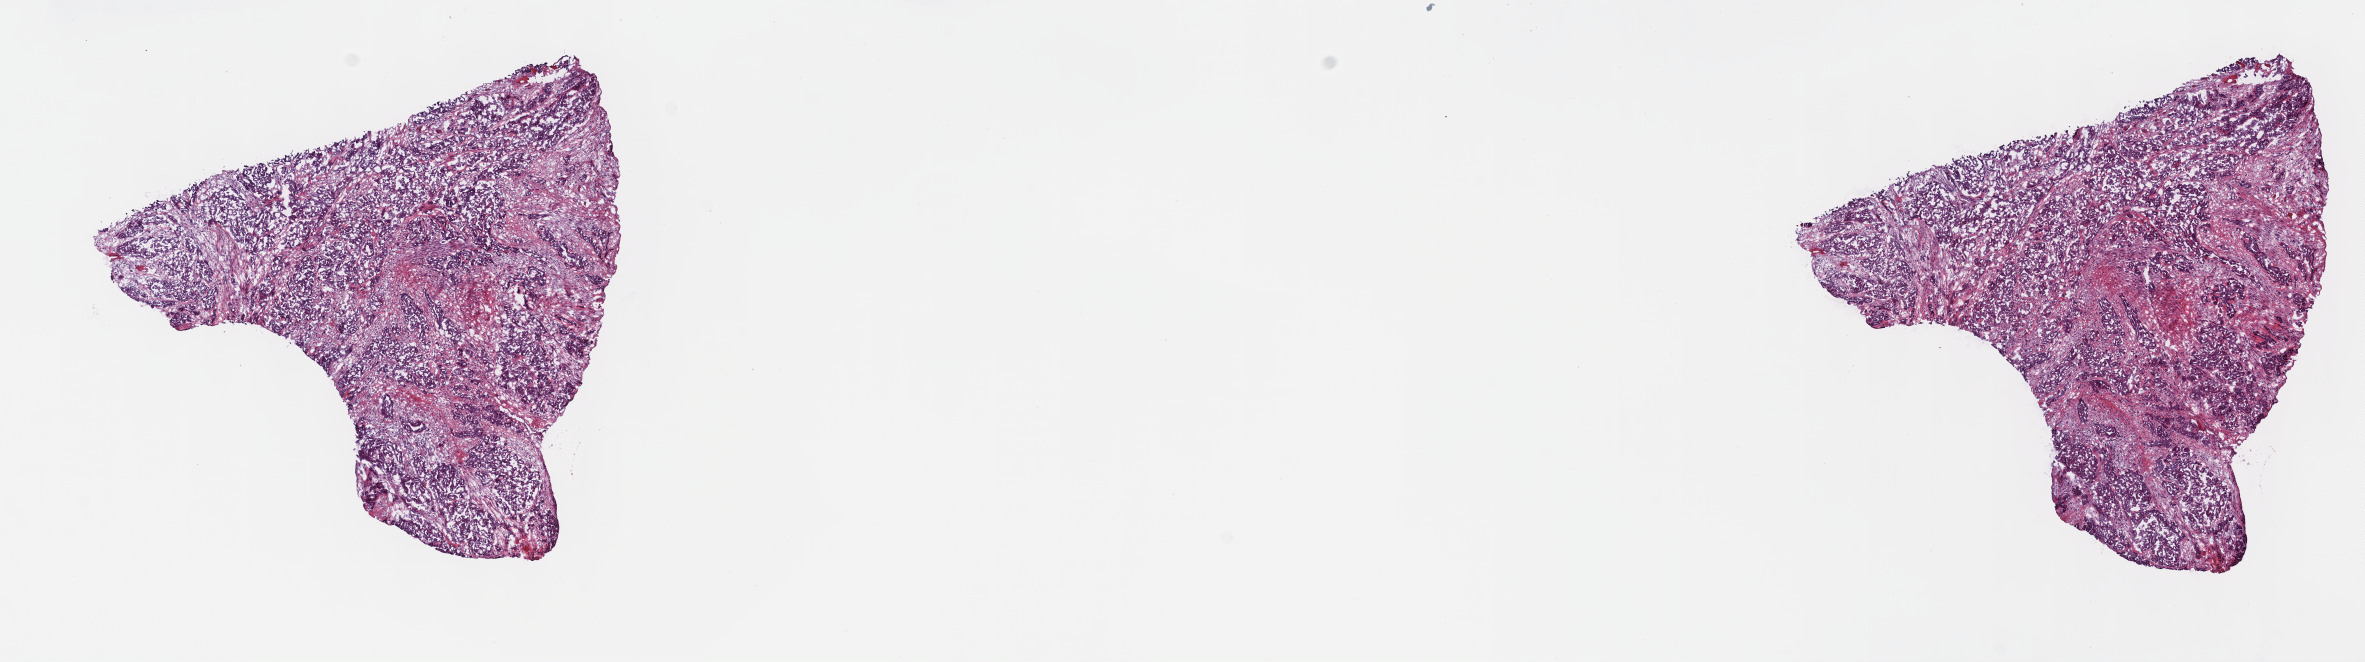
H&E-stained whole-slide image, shown as a low-resolution overview of the whole scanned area (about 19.1 x 5.4 mm, from a 40x scan); frozen section from the top of the tissue portion; sample: primary tumour, mesothelium. Female, age 28 years at initial diagnosis. Slide review estimates, as recorded: tumour cells 100%, tumour nuclei 65%, normal cells 0%, stromal cells 0%, necrosis 0%. Inflammatory infiltration, as recorded: lymphocyte infiltration 1%, monocyte infiltration 0%, neutrophil infiltration 0%.
AJCC pathologic stage: IV. TNM: T4 N3 M0. Pathologic diagnosis: Epithelioid mesothelioma, malignant.